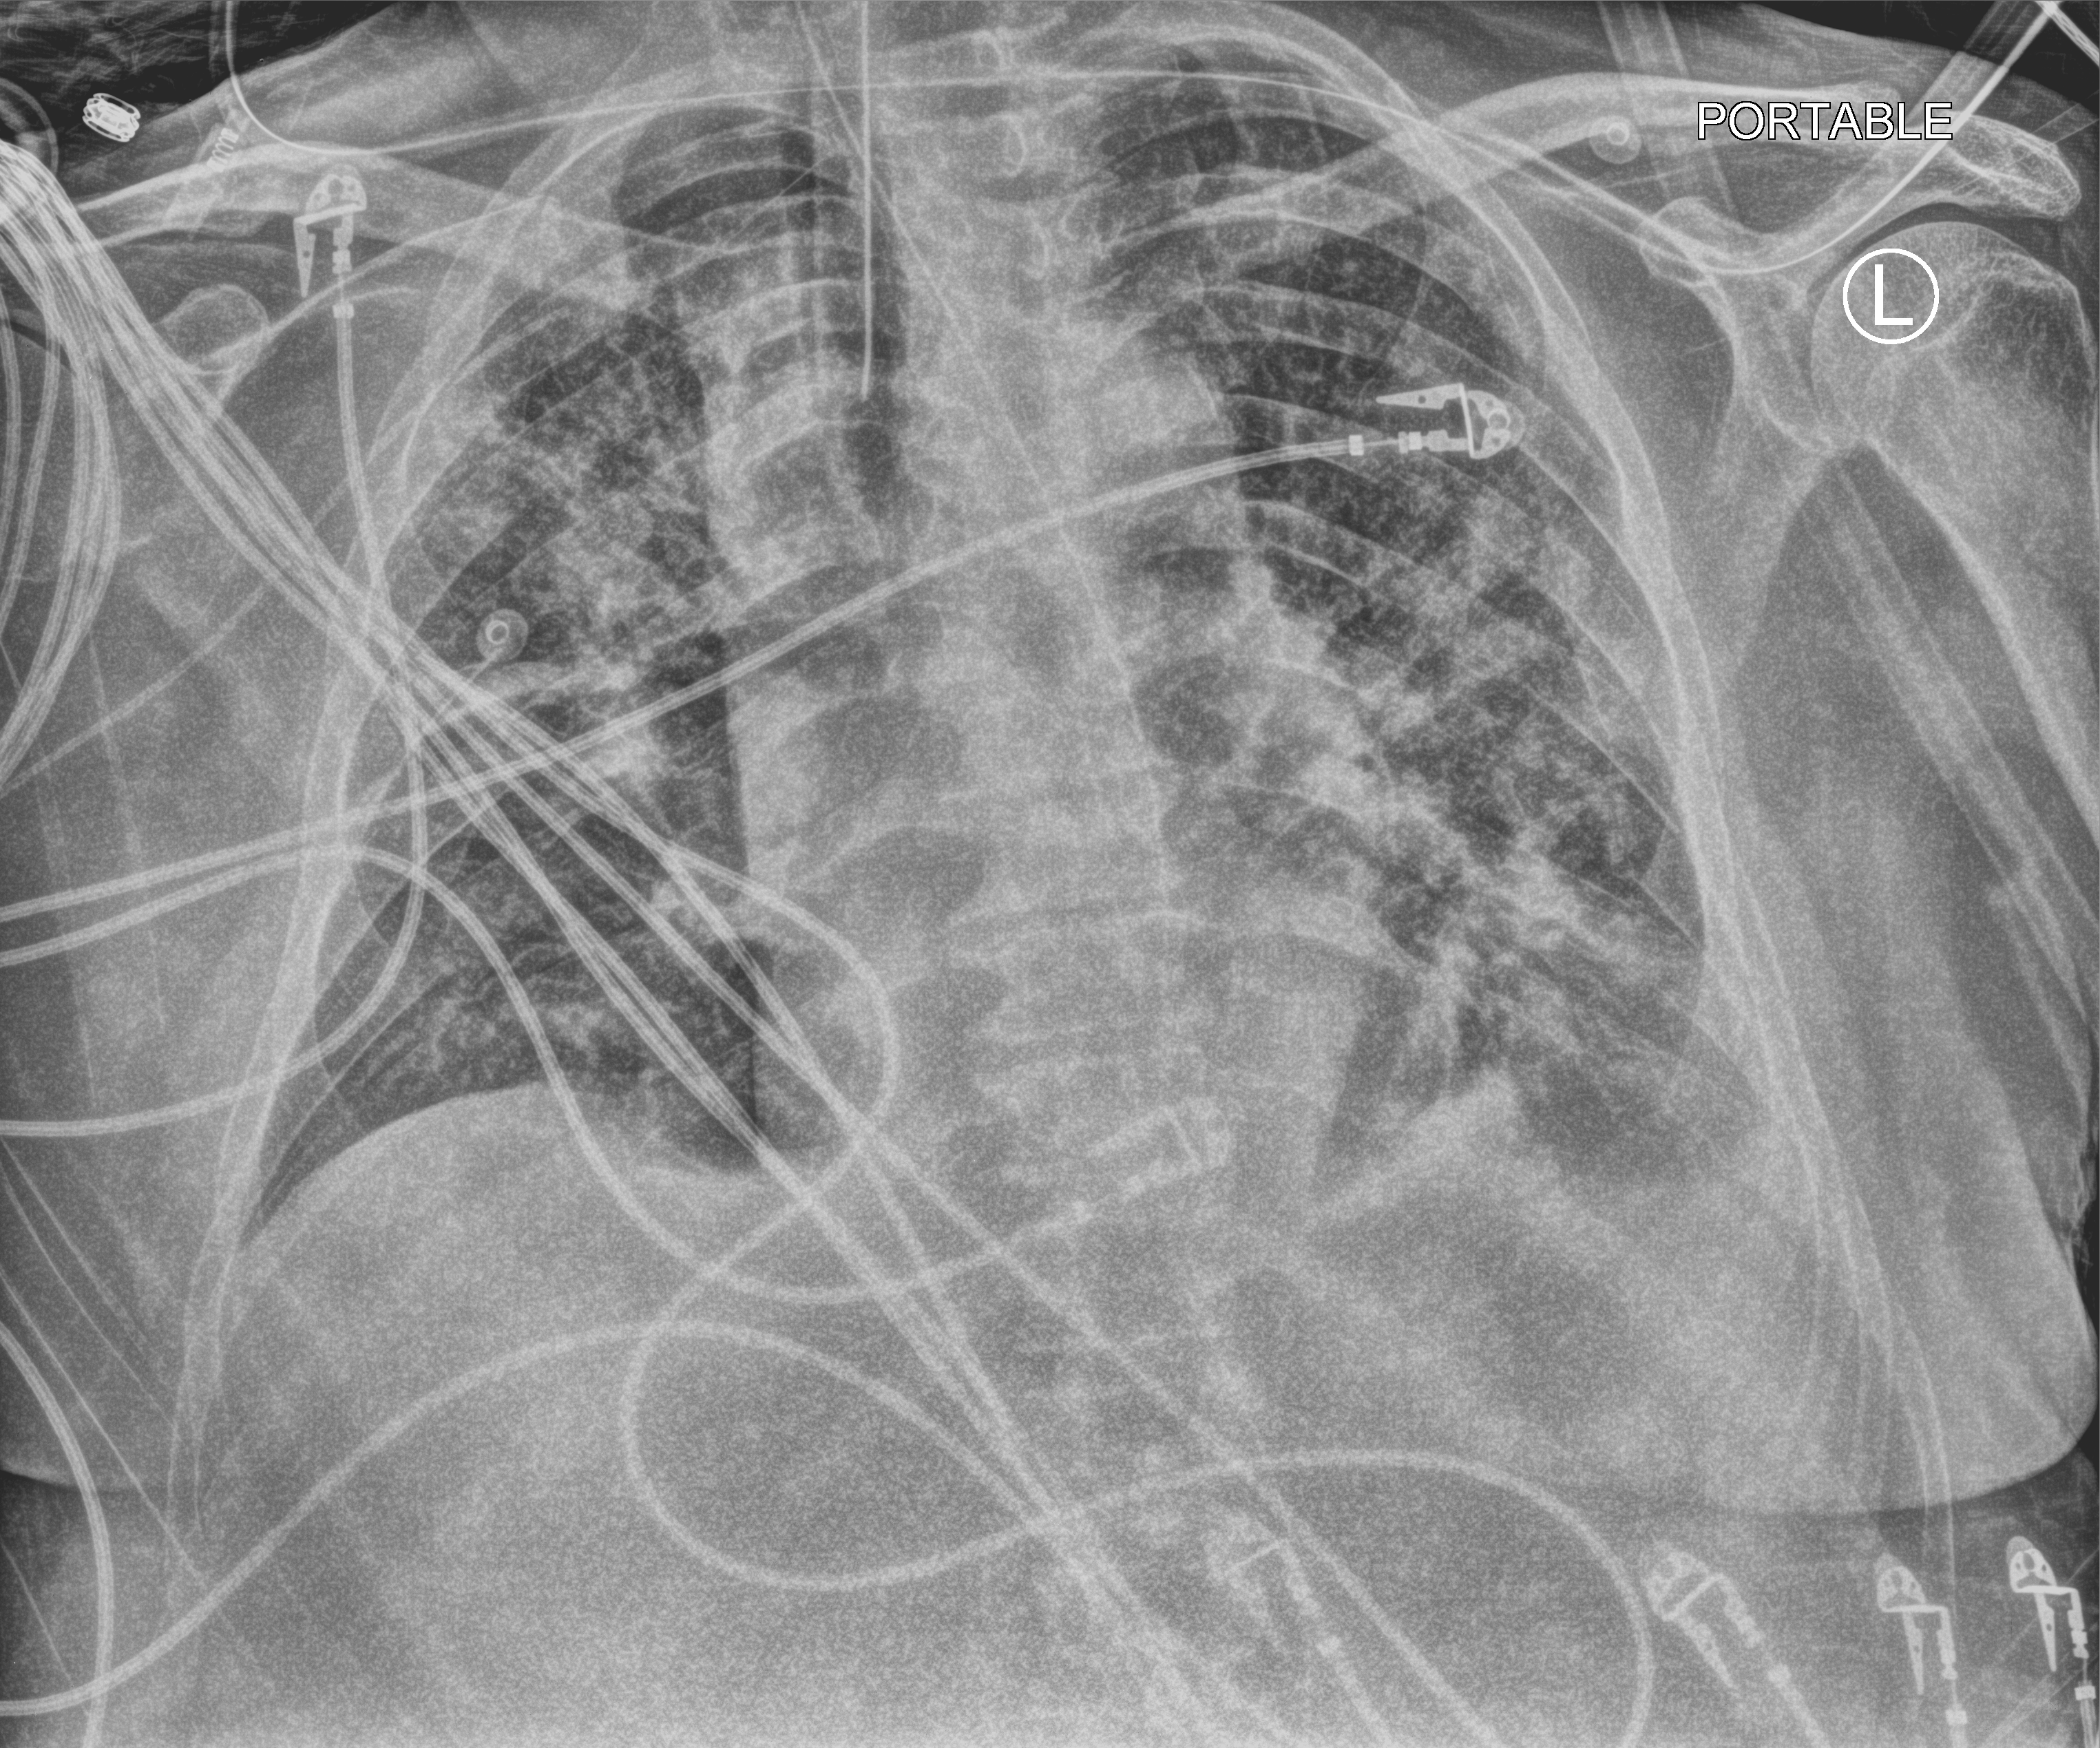
Chest X-ray (portable), anteroposterior (AP) projection. Male patient hospitalised with COVID-19, age 60–74 years.
Hospital-stay facts (about this admission, not read from this image; timing relative to this image not recorded): admitted to intensive care during this hospital stay: yes.